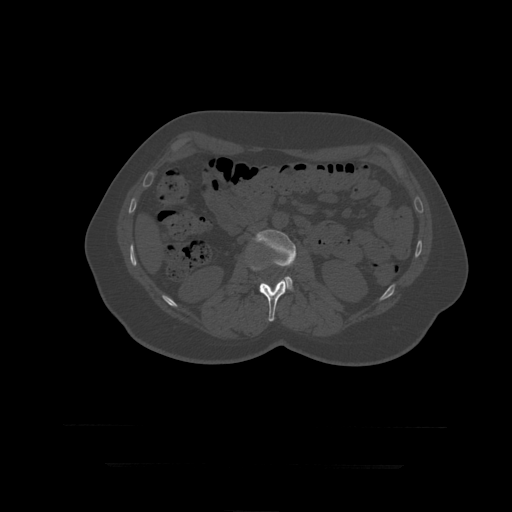
CT including the spine, one axial slice; position 139 of 399 along the scan axis; reconstruction kernel STANDARD; bone window (W 1800 / L 400 HU); 512 × 512 image matrix. Patient age 41 years. From the clinical record (not read from this slice): primary cancer: breast.
Structures marked on this image (semi-automatic segmentation, software-assisted and operator-edited):
- L2 vertebra: box from (x=251, y=266) to (x=288, y=322) px
- L3 vertebra: (x=253, y=230)–(x=297, y=291)